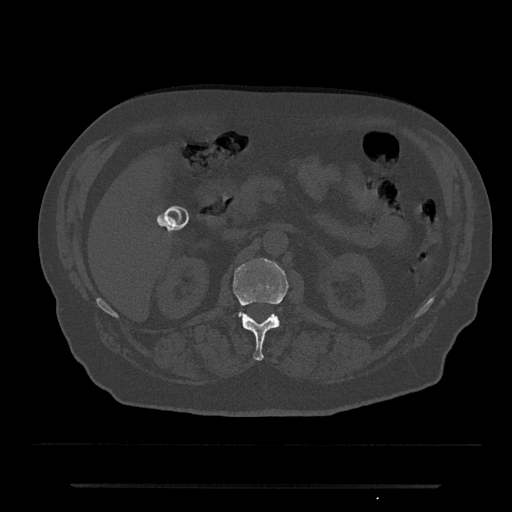
CT including the spine, one axial slice. Position 526 of 797 along the scan axis. Reconstruction kernel Br40s/3. 120 kVp. Bone window (W 1800 / L 400 HU). 0.5 mm slice thickness. 512 × 512 image matrix, field of view 434 × 434 mm. Male patient, age 80 years. Case-level facts recorded for this patient, not image findings: primary cancer: prostate; vertebrae with lytic lesions (as recorded): L1, T11.
Outlined on this slice (semi-automatically segmented with operator editing):
- L1 vertebra: bounding box [x1, y1, x2, y2] px = [232, 258, 289, 361]